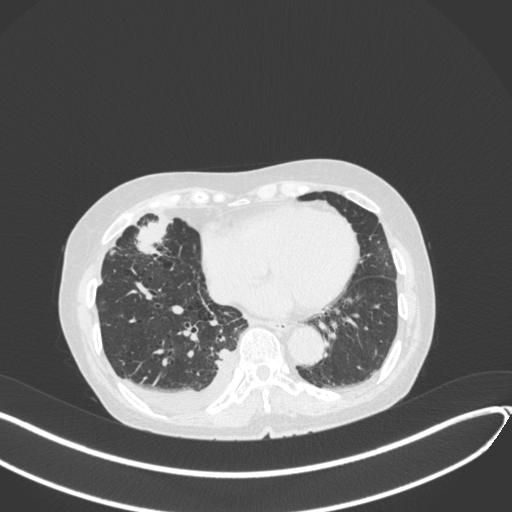
Chest CT, one axial slice; slice 130 of 418 in the series (ordered by position); reconstruction kernel B31f; lung window (W 1500 / L -600 HU); 1 mm slice thickness; 512 × 512 image matrix, field of view 400 × 400 mm. Female patient, age 75 years. From the clinical record (not read from this slice): clinical TNM (as recorded): T2a N3 M0.
Structures marked on this image (bounding box drawn by a radiologist):
- lung tumour (recorded histology: adenocarcinoma): bounding box <130,218,180,260> (left, top, right, bottom; pixels)